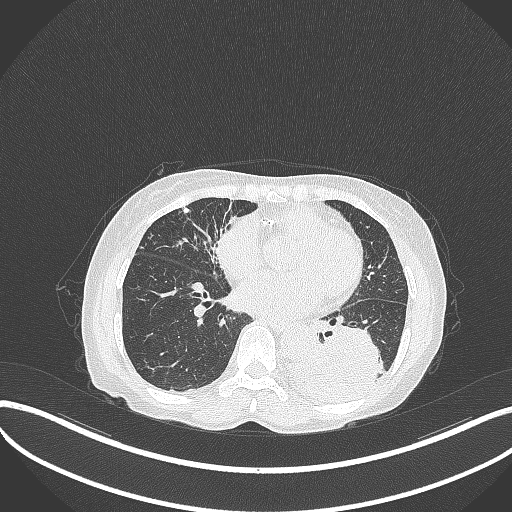
Chest CT, one axial slice. Slice 125 of 370 in the series (ordered by position). Reconstruction kernel B70f. Lung window (W 1500 / L -600 HU). 512 × 512 image matrix. Female patient, age 78 years. From the clinical record (not read from this slice): clinical TNM (as recorded): T3 N0 M1.
Structures marked on this image (bounding box drawn by a radiologist):
- lung tumour (recorded histology: squamous cell carcinoma): bounding box <289,318,388,406> (left, top, right, bottom; pixels)